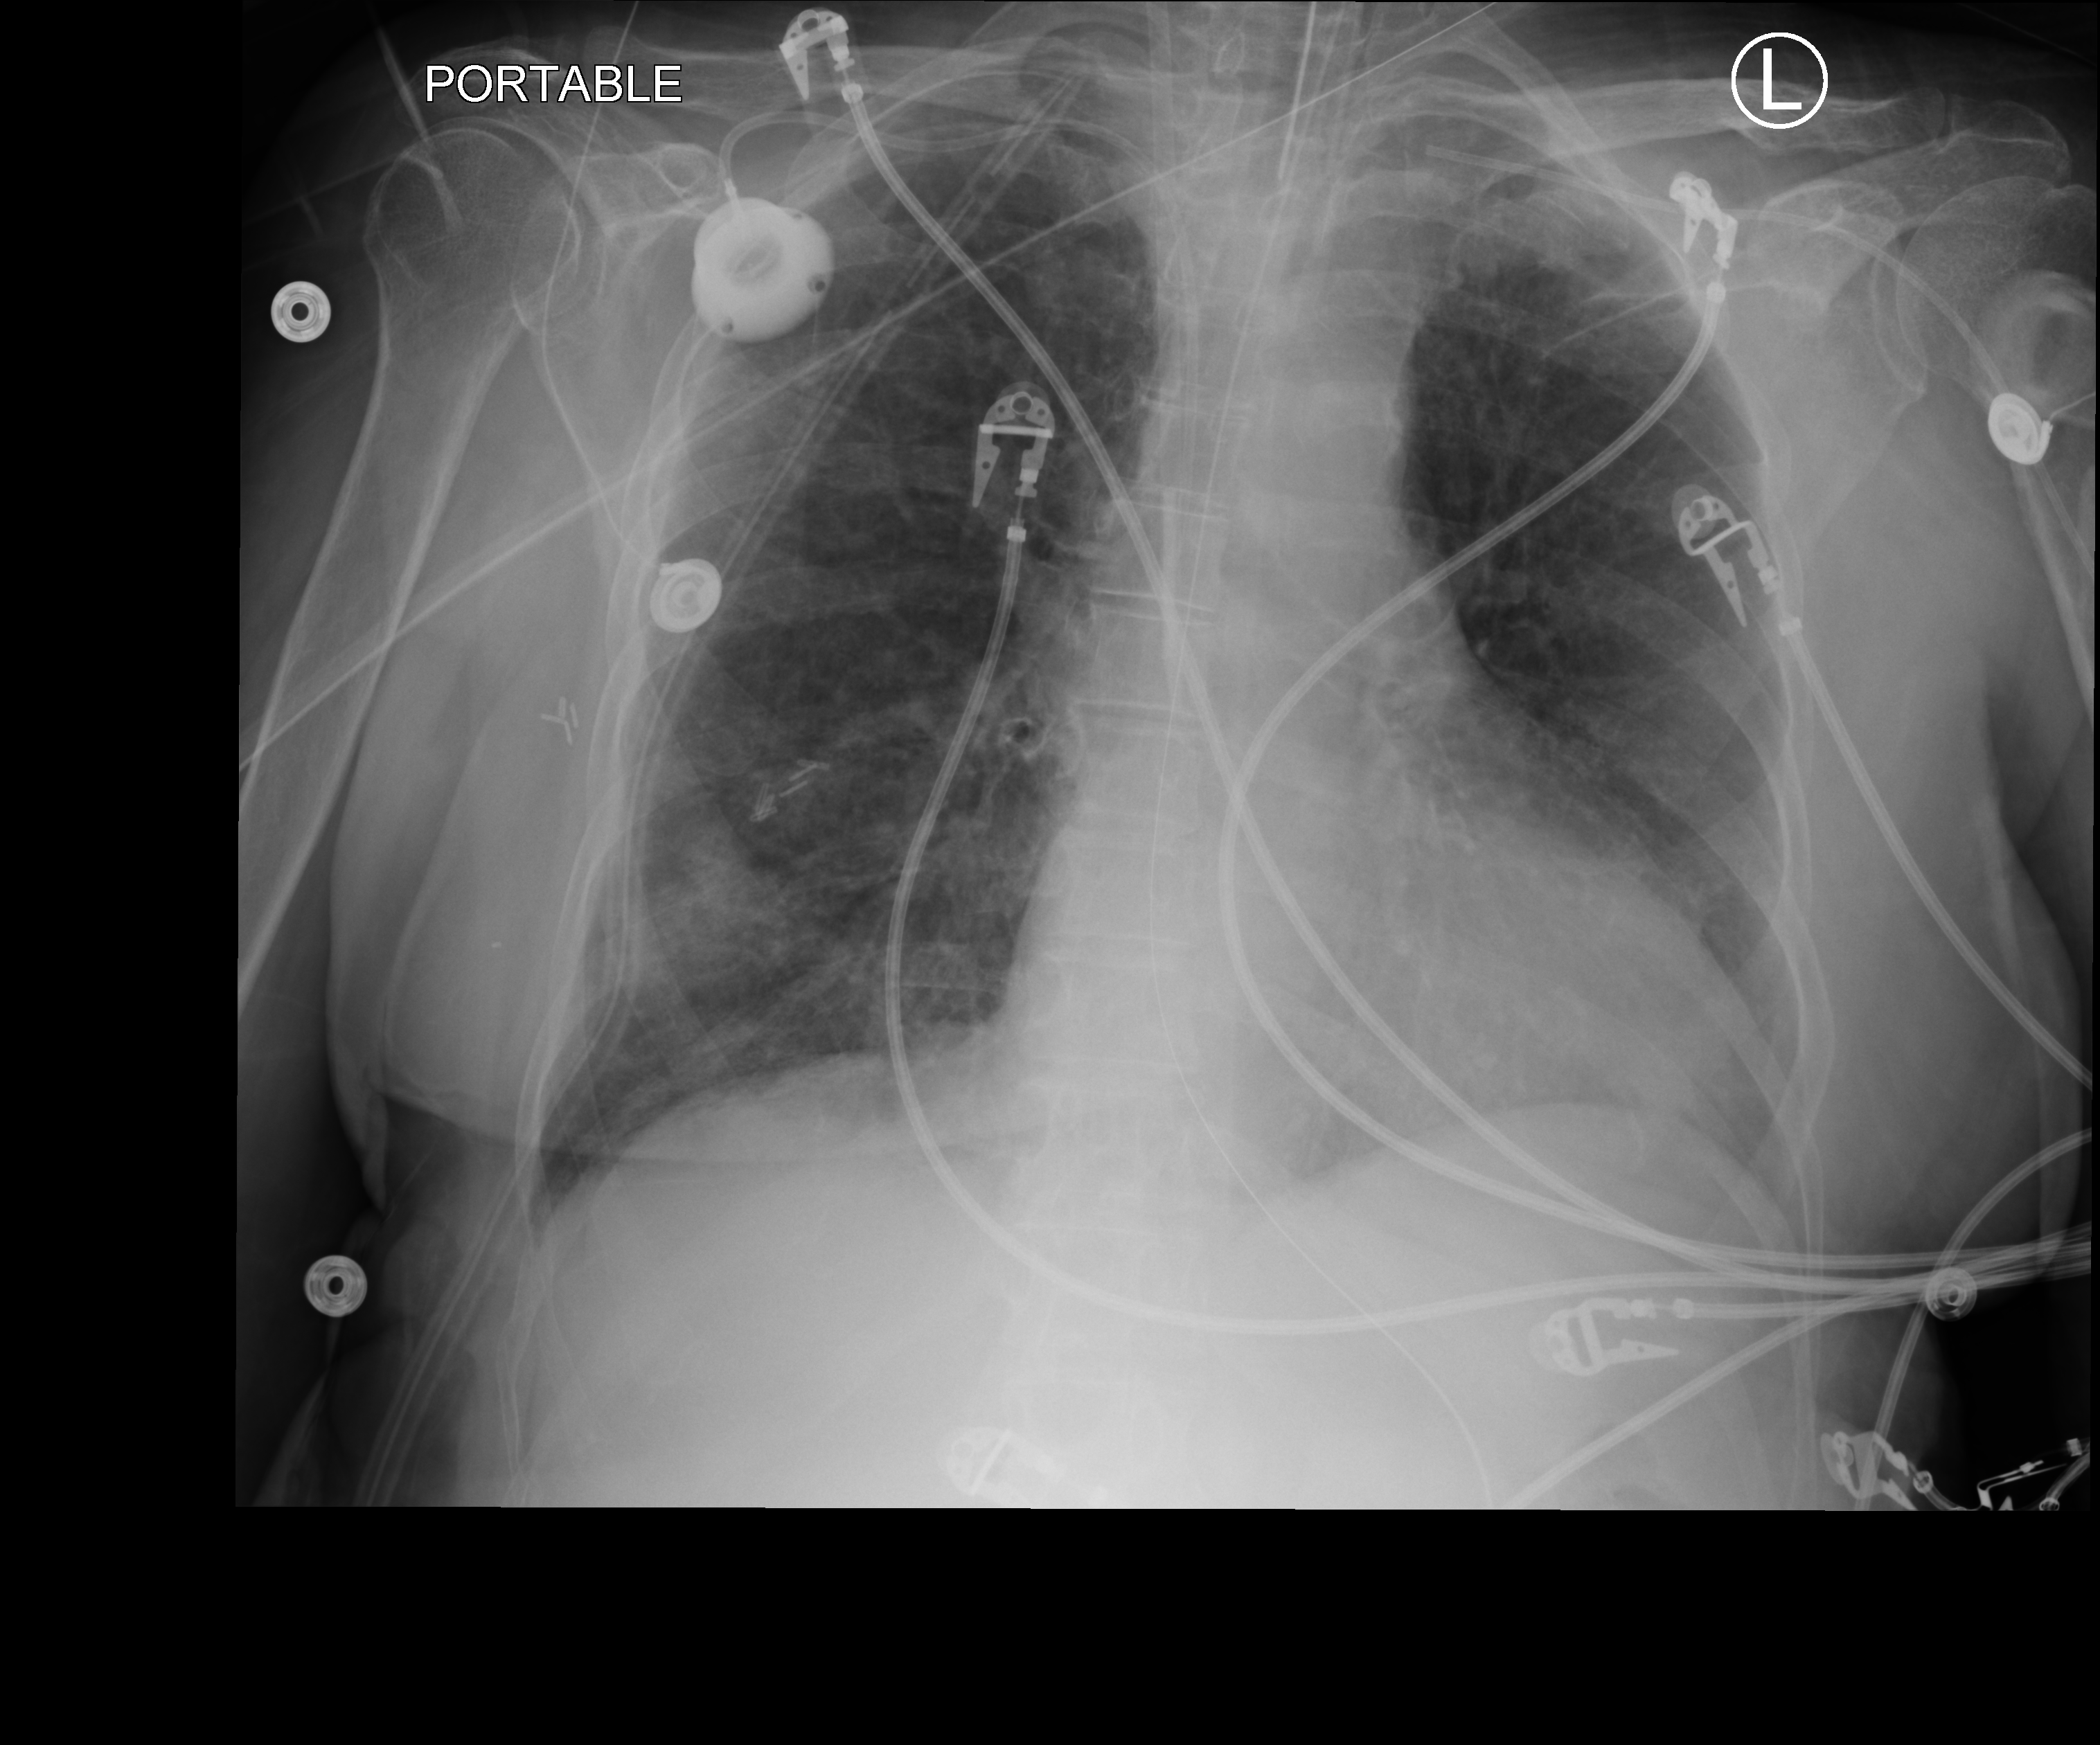
Bedside chest radiograph (computed radiography), anteroposterior (AP) projection. Patient hospitalised with COVID-19; female, aged 60–74 years.
Admission-level facts for this patient (not findings on this image; timing relative to this image not recorded): length of hospital stay: 43 days; chronic kidney disease (admission record): no; mechanically ventilated during this hospital stay: yes.